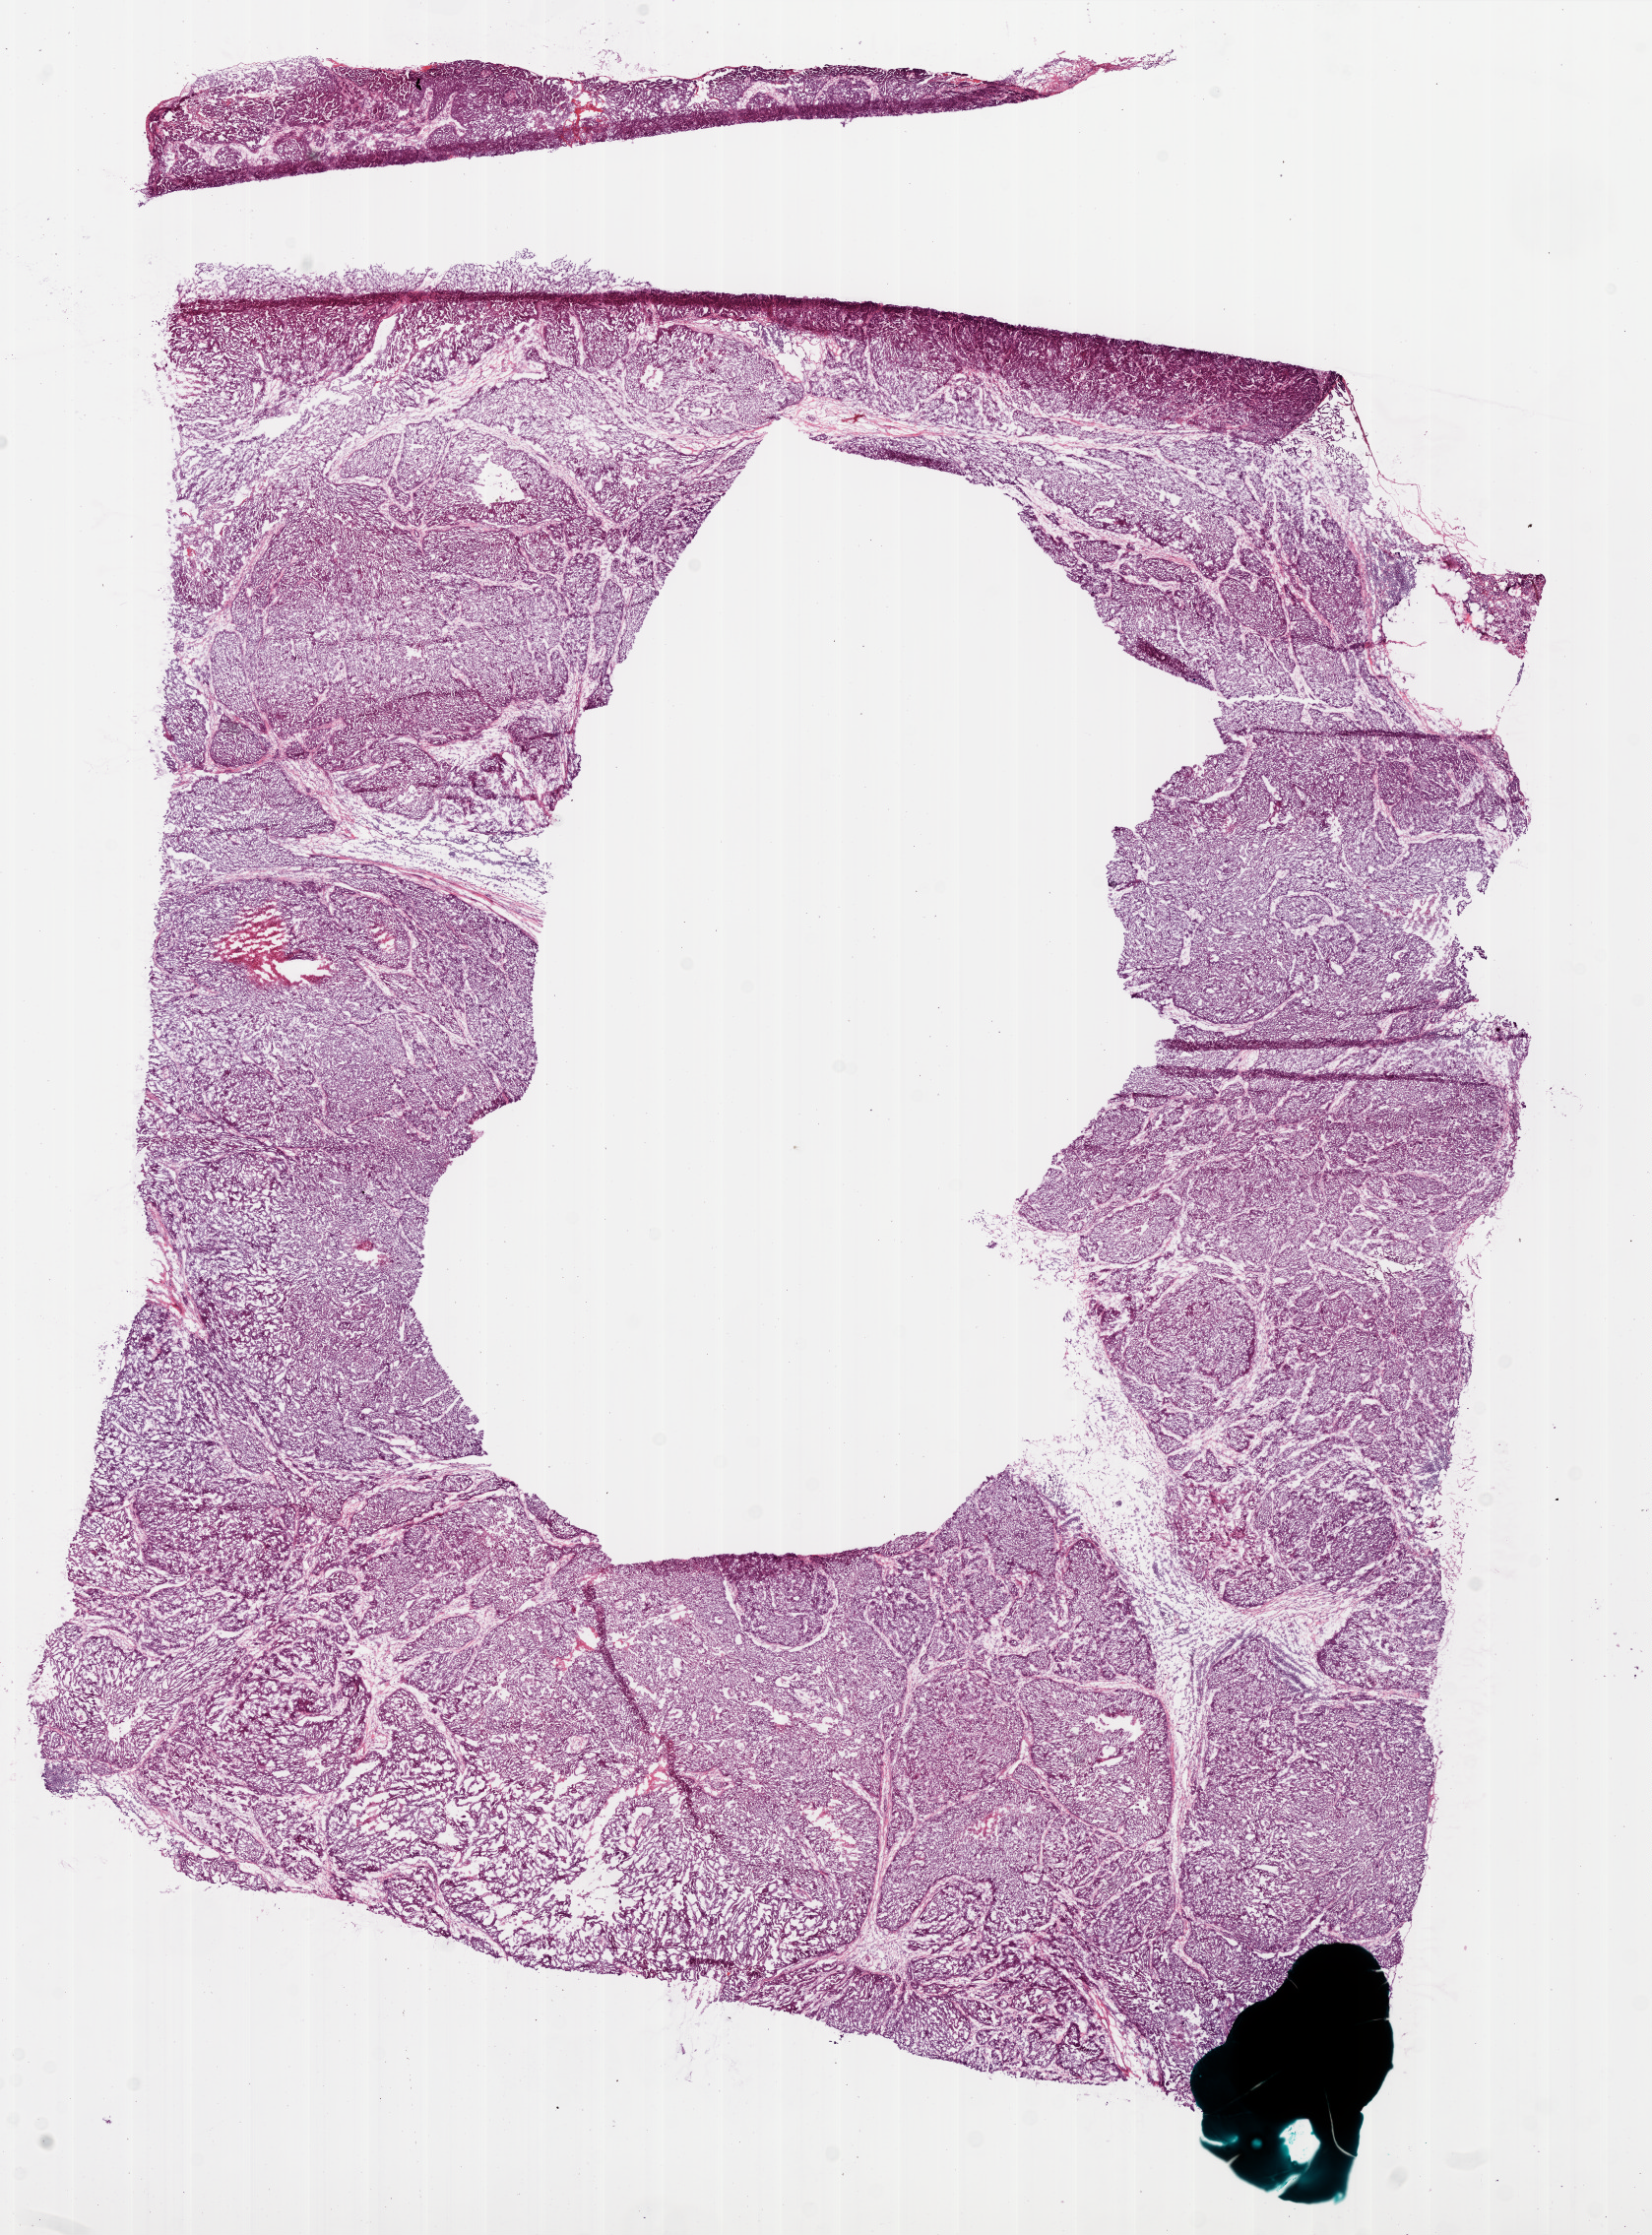
Whole-slide histology image, H&E-stained — whole scanned area (about 13.5 x 18.3 mm, acquisition: 20x scan) shown as a low-resolution overview, frozen section from the bottom of the tissue portion, sample: primary tumour, ovary. Female, age 49 years at initial diagnosis. Histologic grade: G3 (poorly differentiated). Slide review estimates, as recorded: tumour cells 90%, tumour nuclei 98%, normal cells 0%, stromal cells 10%, necrosis 0%.
Pathologic diagnosis: Serous cystadenocarcinoma, NOS. FIGO stage: IIIC.